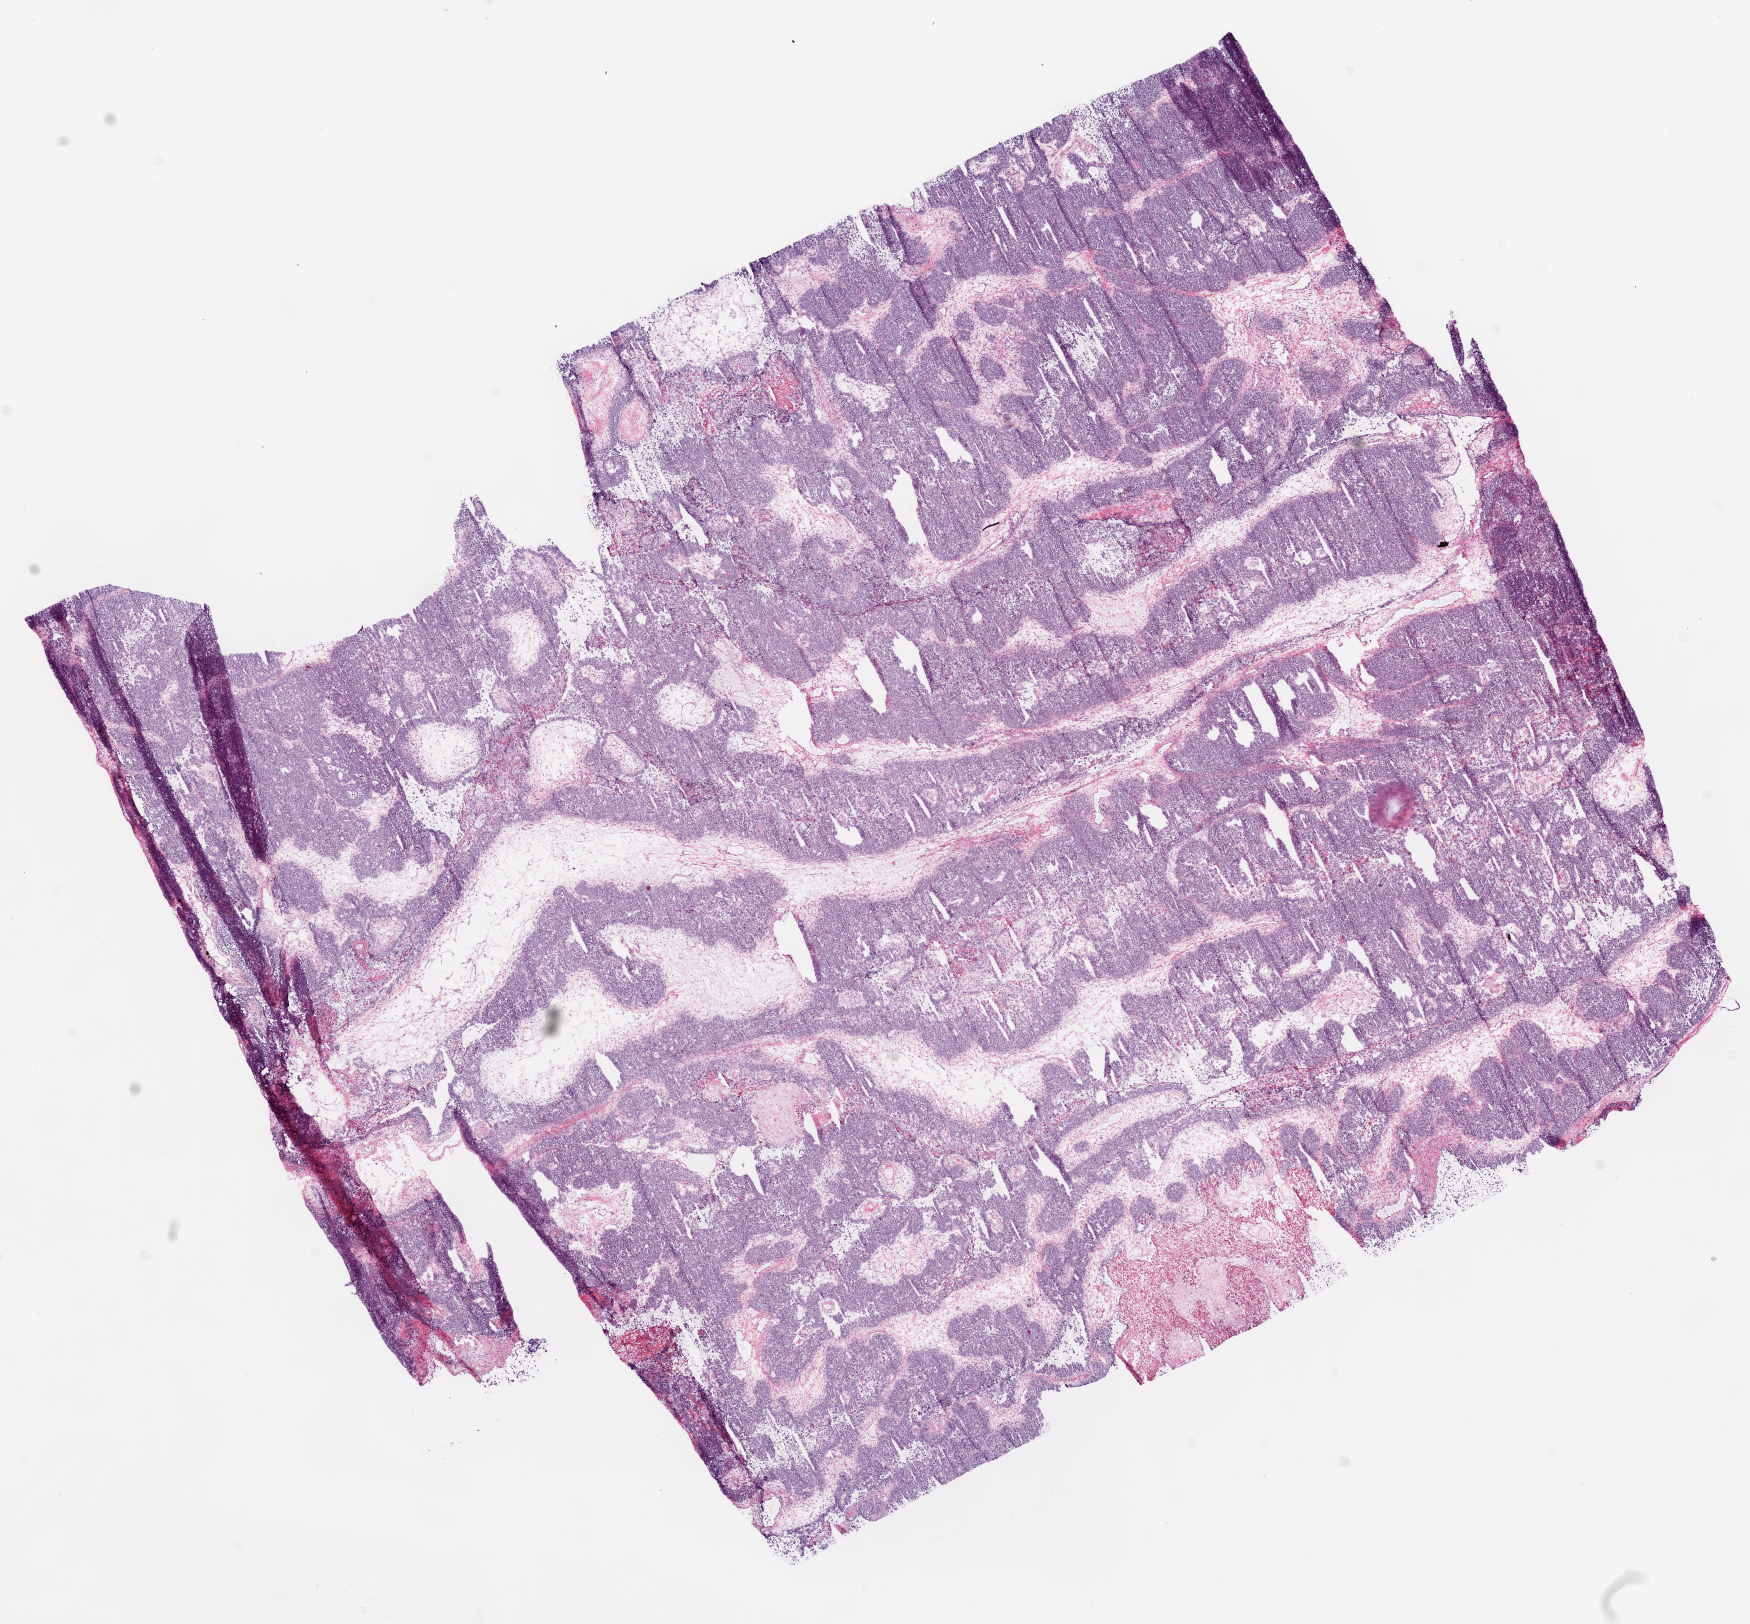
Whole-slide histology image, H&E — whole scanned area (about 14.0 x 13.0 mm, from a 20x scan) shown as a low-resolution overview, frozen section from the bottom of the tissue portion, sample: primary tumour, ovary. Female patient; age at initial diagnosis 64 years. Histologic grade: G3 (poorly differentiated). Slide review estimates, as recorded: tumour cells 72%, tumour nuclei 80%, normal cells 0%, stromal cells 20%, necrosis 8%.
* pathologic diagnosis: Serous cystadenocarcinoma, NOS
* FIGO stage: IIC
* laterality: bilateral